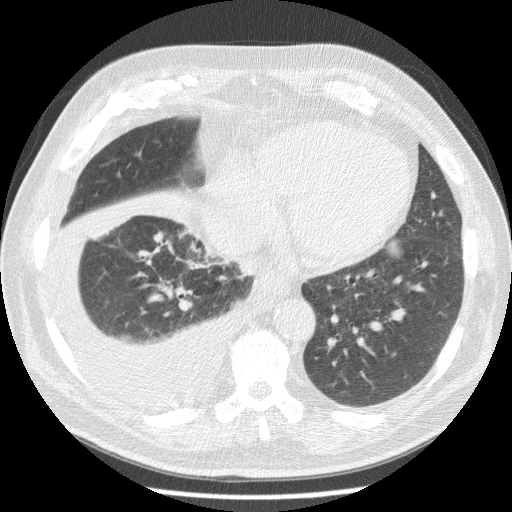
Low-dose screening chest CT, one axial slice. Slice 65 of 180 in the series (ordered by position). Reconstruction kernel STANDARD. 120 kVp. Lung window (W 1500 / L -600 HU). 512 × 512 image matrix, field of view 355 × 355 mm.
Annotated regions visible in this slice (outlined manually by an expert reader):
- lesion 1 (tumor, lower lobe of left lung): box from (x=389, y=241) to (x=397, y=254) px